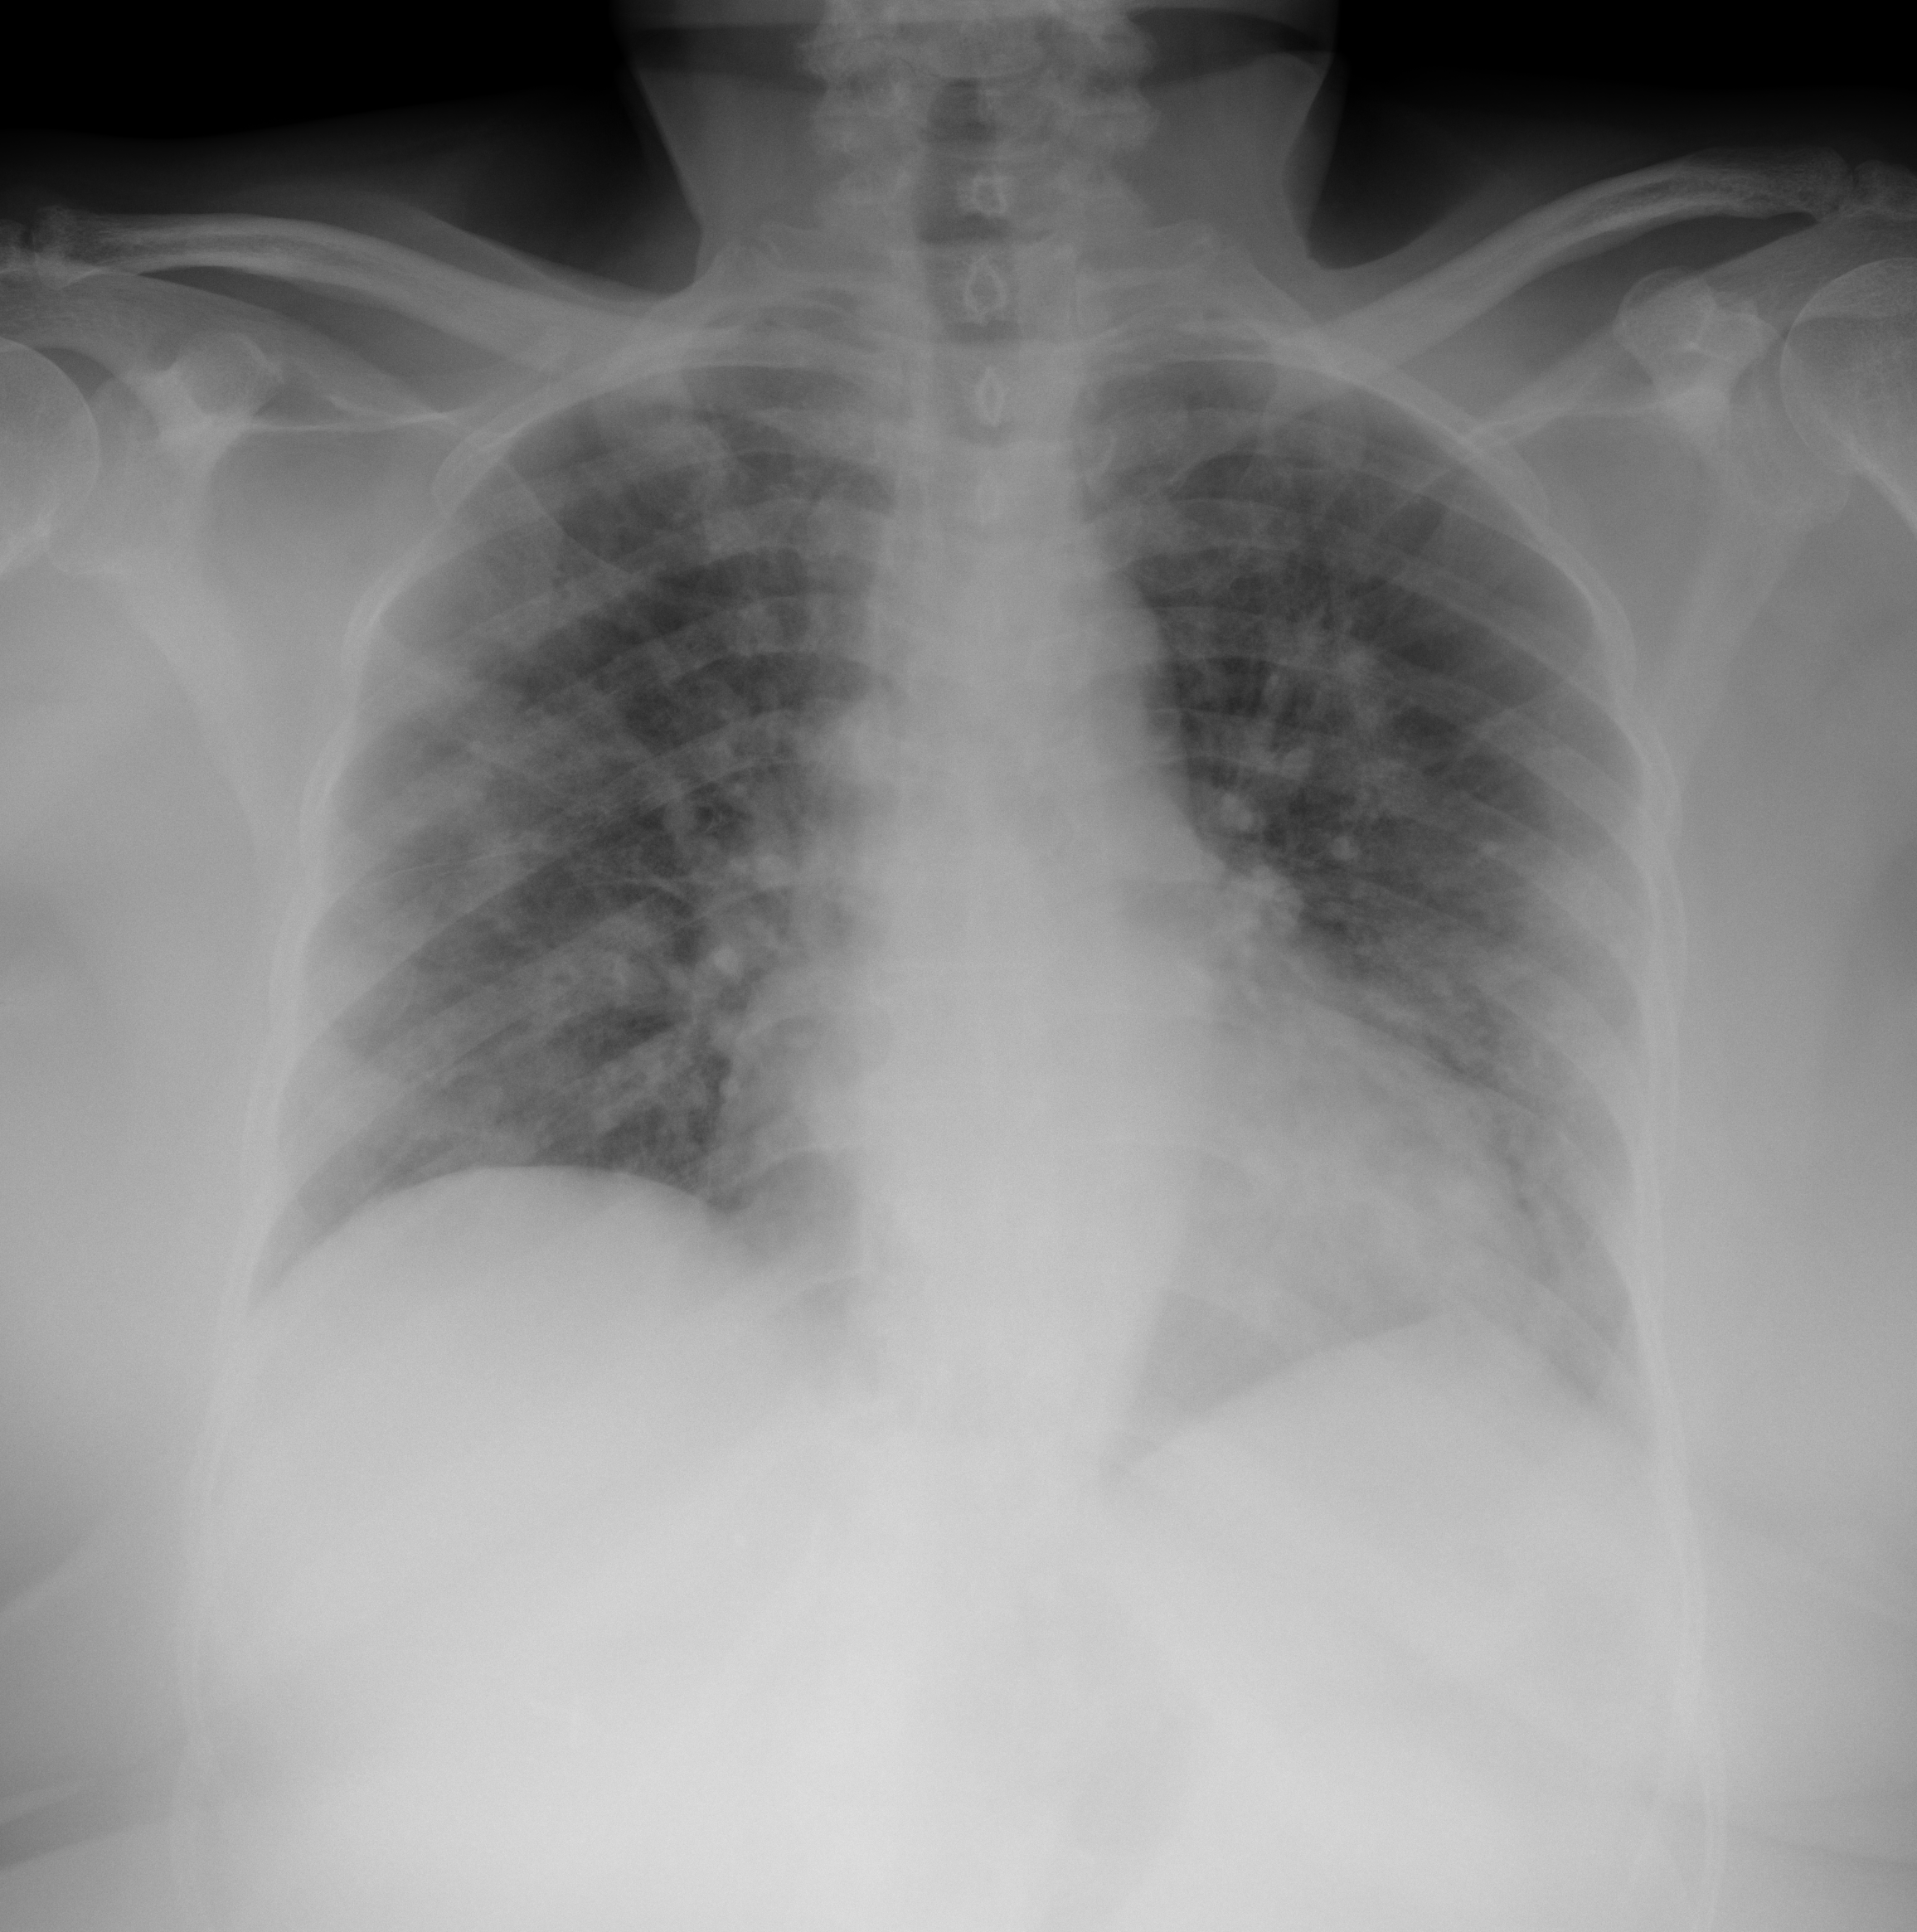
Chest X-ray (portable), AP projection. Female patient, age 73 years; imaged 5 days after the COVID-19 diagnosis.
Radiologist key findings (as recorded): Patchy infiltrates in both lungs mainly in the periphery bilaterally.